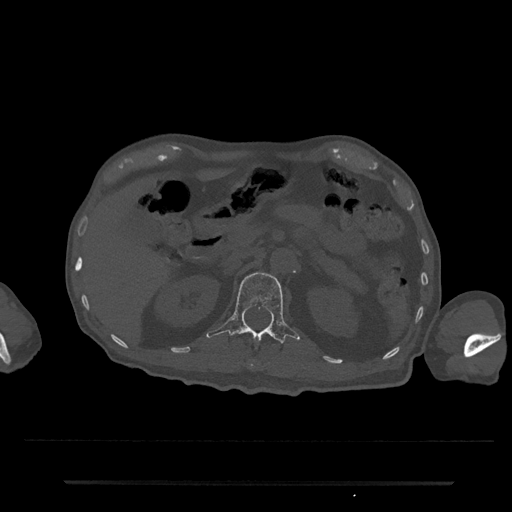
CT including the spine, one axial slice. Slice 139 of 797 in the series (ordered by position). 120 kVp. Bone window (W 1800 / L 400 HU). 0.5 mm slice thickness. 512 × 512 image matrix, field of view 427 × 427 mm. Patient: male, 74 years. Case-level facts recorded for this patient, not image findings: primary cancer: prostate.
Outlined on this slice (semi-automatic segmentation, software-assisted and operator-edited):
- L1 vertebra: box from (x=206, y=272) to (x=300, y=344) px
- T12 vertebra: (x=249, y=361)–(x=255, y=368)